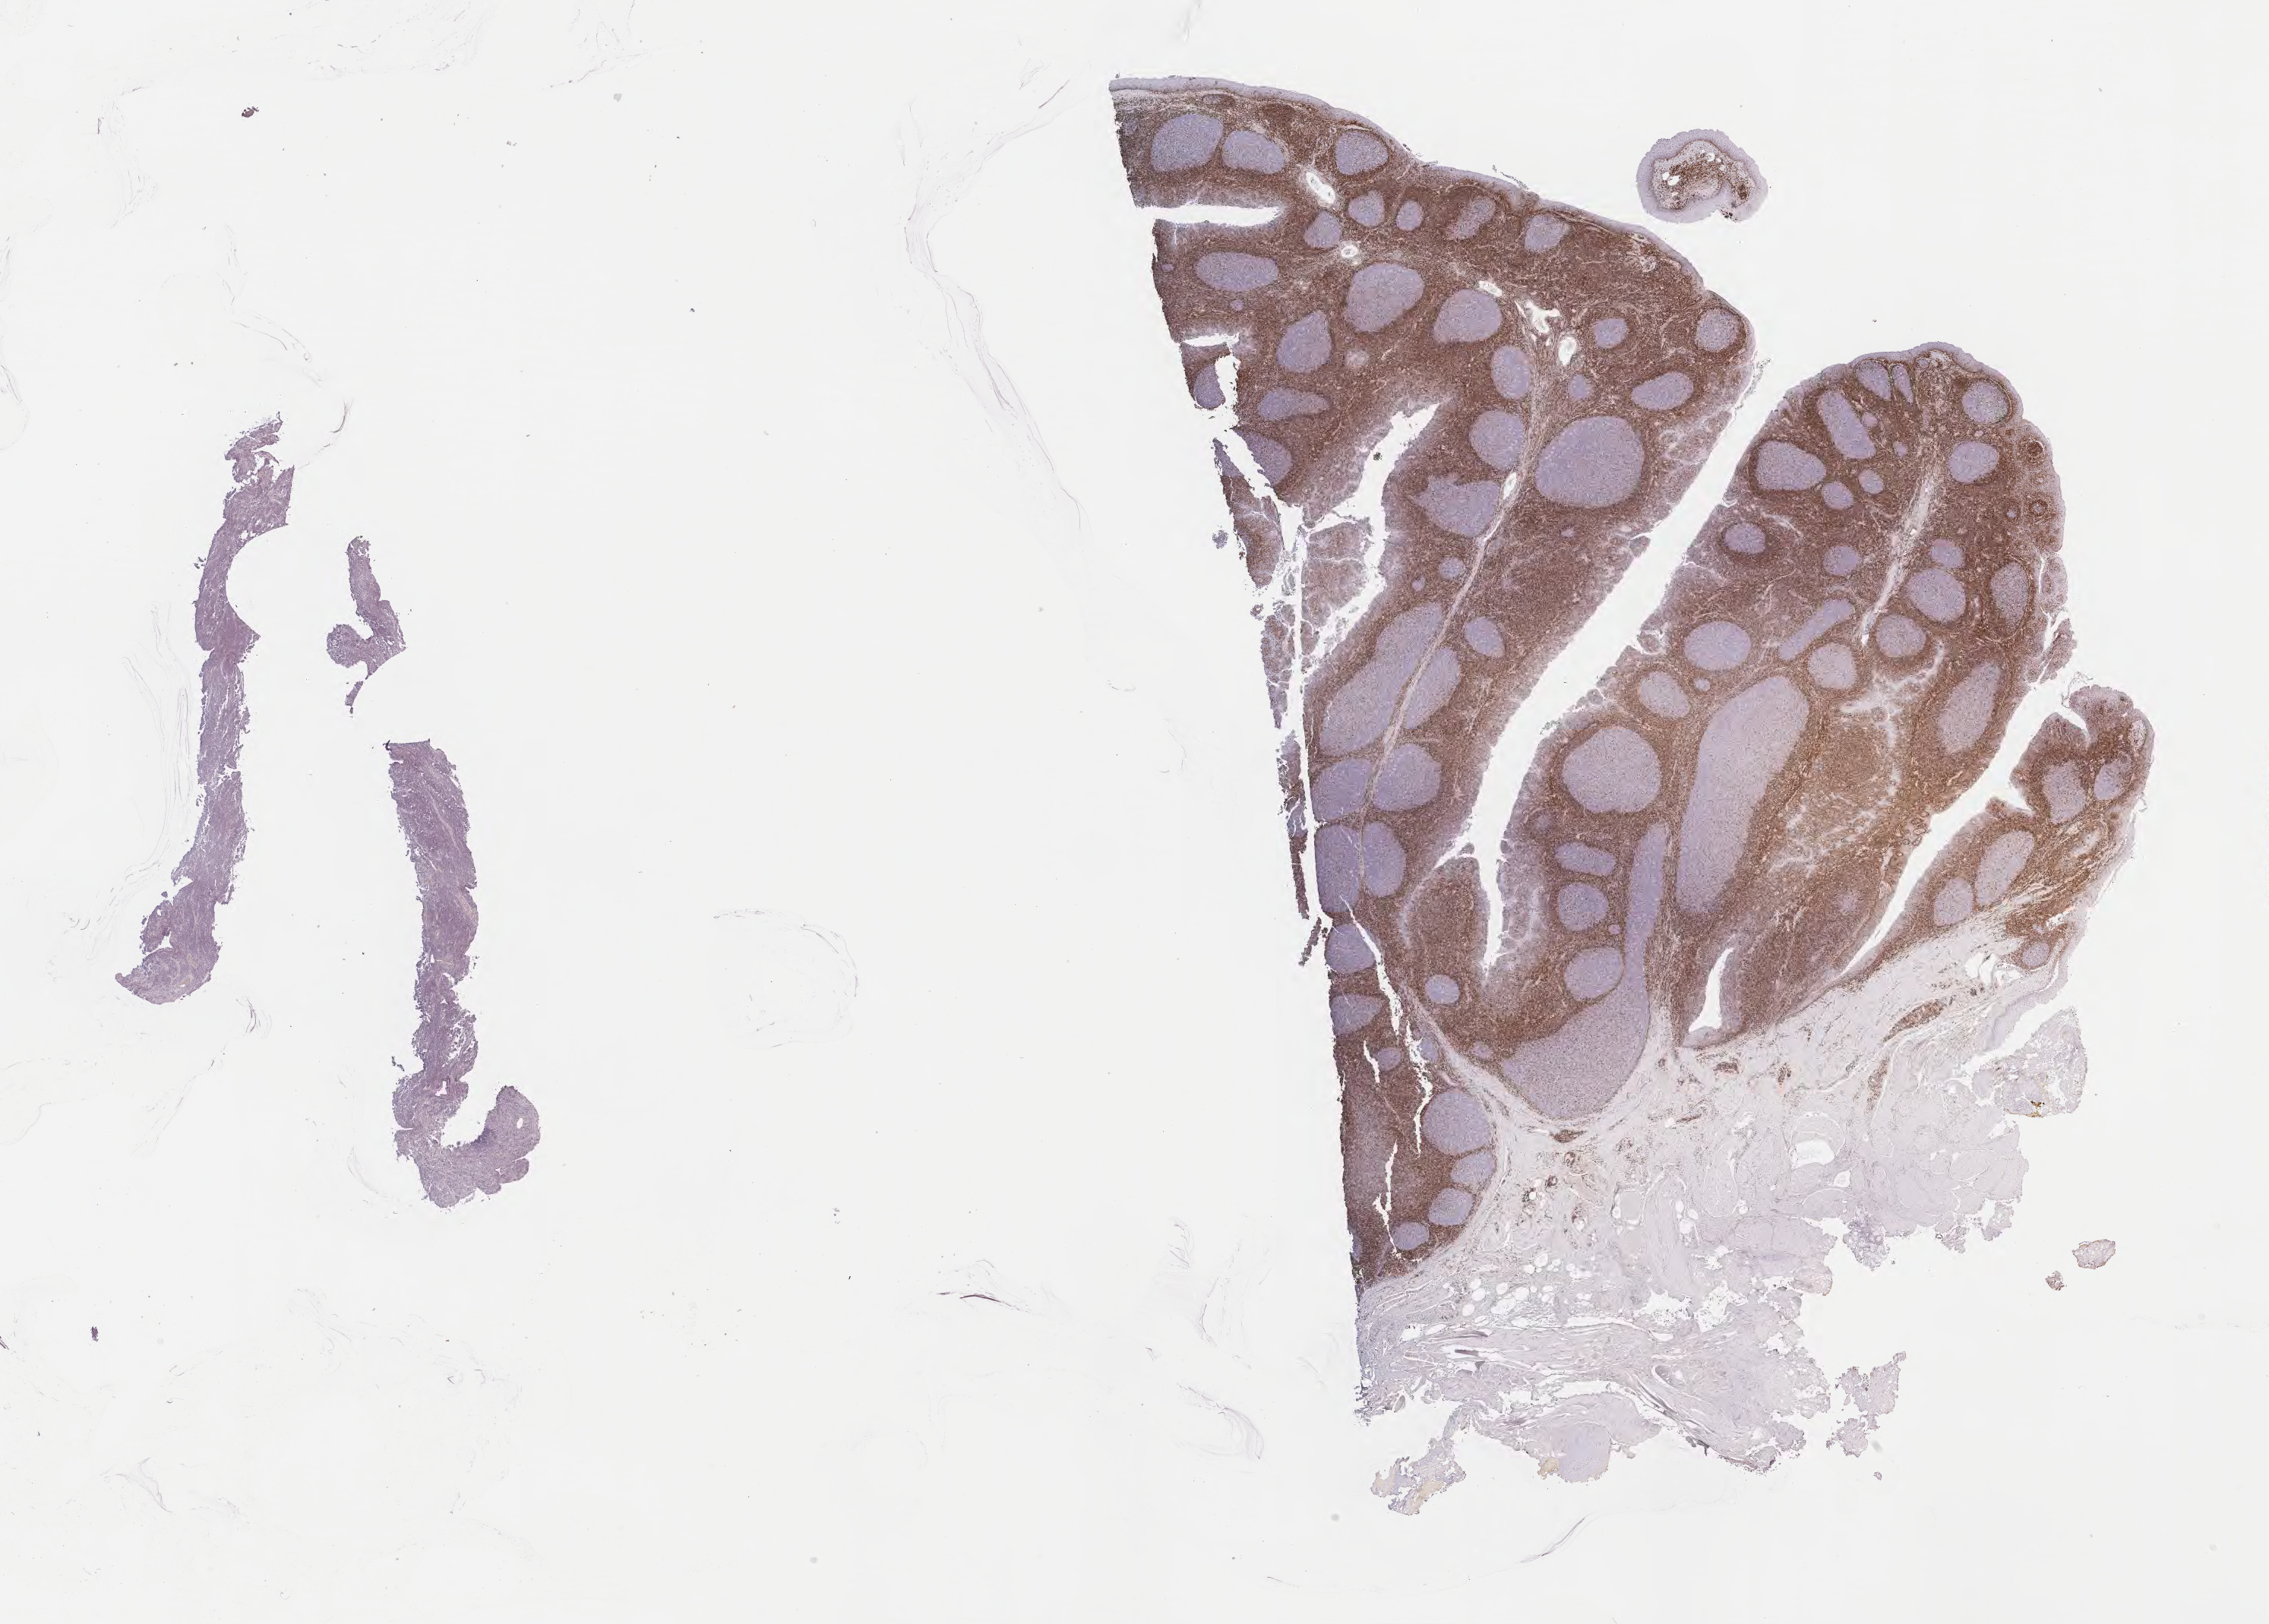
IHC for BCL2, whole-slide image — low-resolution overview of the scanned area, about 24.2 x 17.3 mm; tumor tissue; site: spleen. Patient: male, age at initial diagnosis 6 years.
Diagnosis: Burkitt lymphoma, NOS.